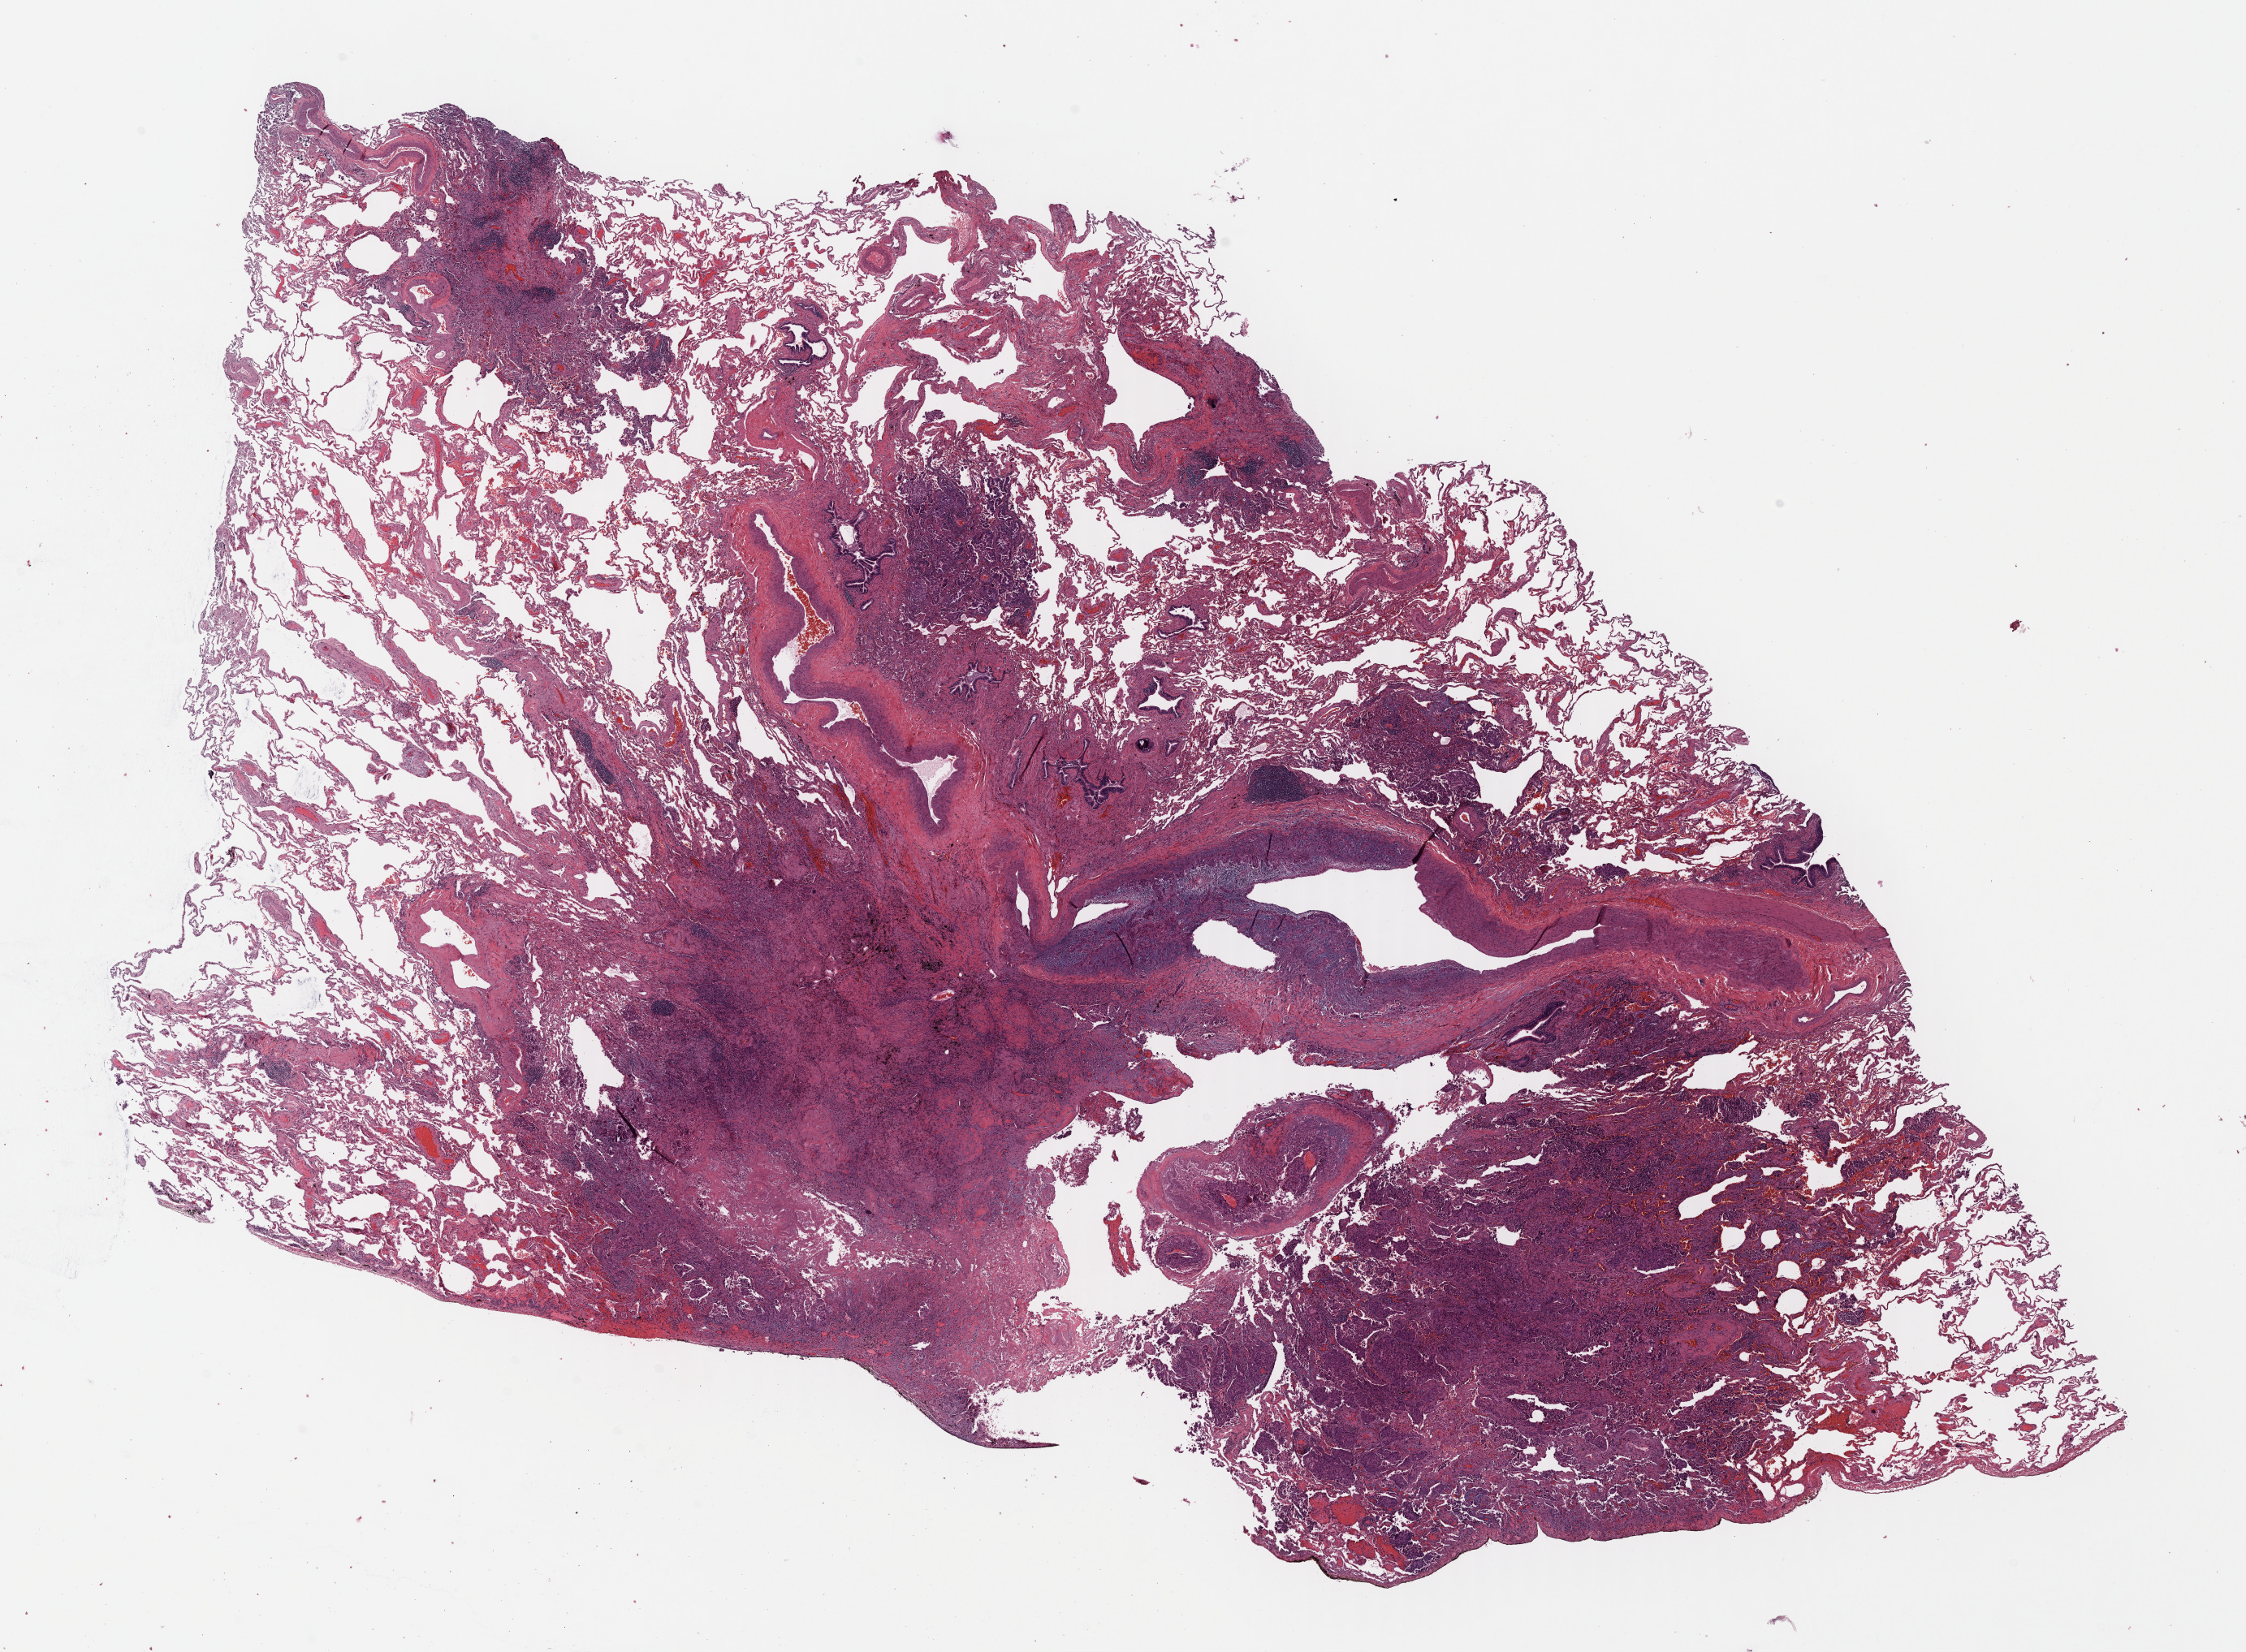
Whole-slide histology image, H&E-stained, low-resolution overview of the scanned area, about 21.7 x 16.0 mm (acquisition: 40x scan); formalin-fixed paraffin-embedded (FFPE) diagnostic section; sample: primary tumour, lung. Patient: male, age at initial diagnosis 67 years.
• laterality: right
• pathologic diagnosis: Adenocarcinoma, NOS (upper lobe, lung)
• AJCC pathologic stage: IA